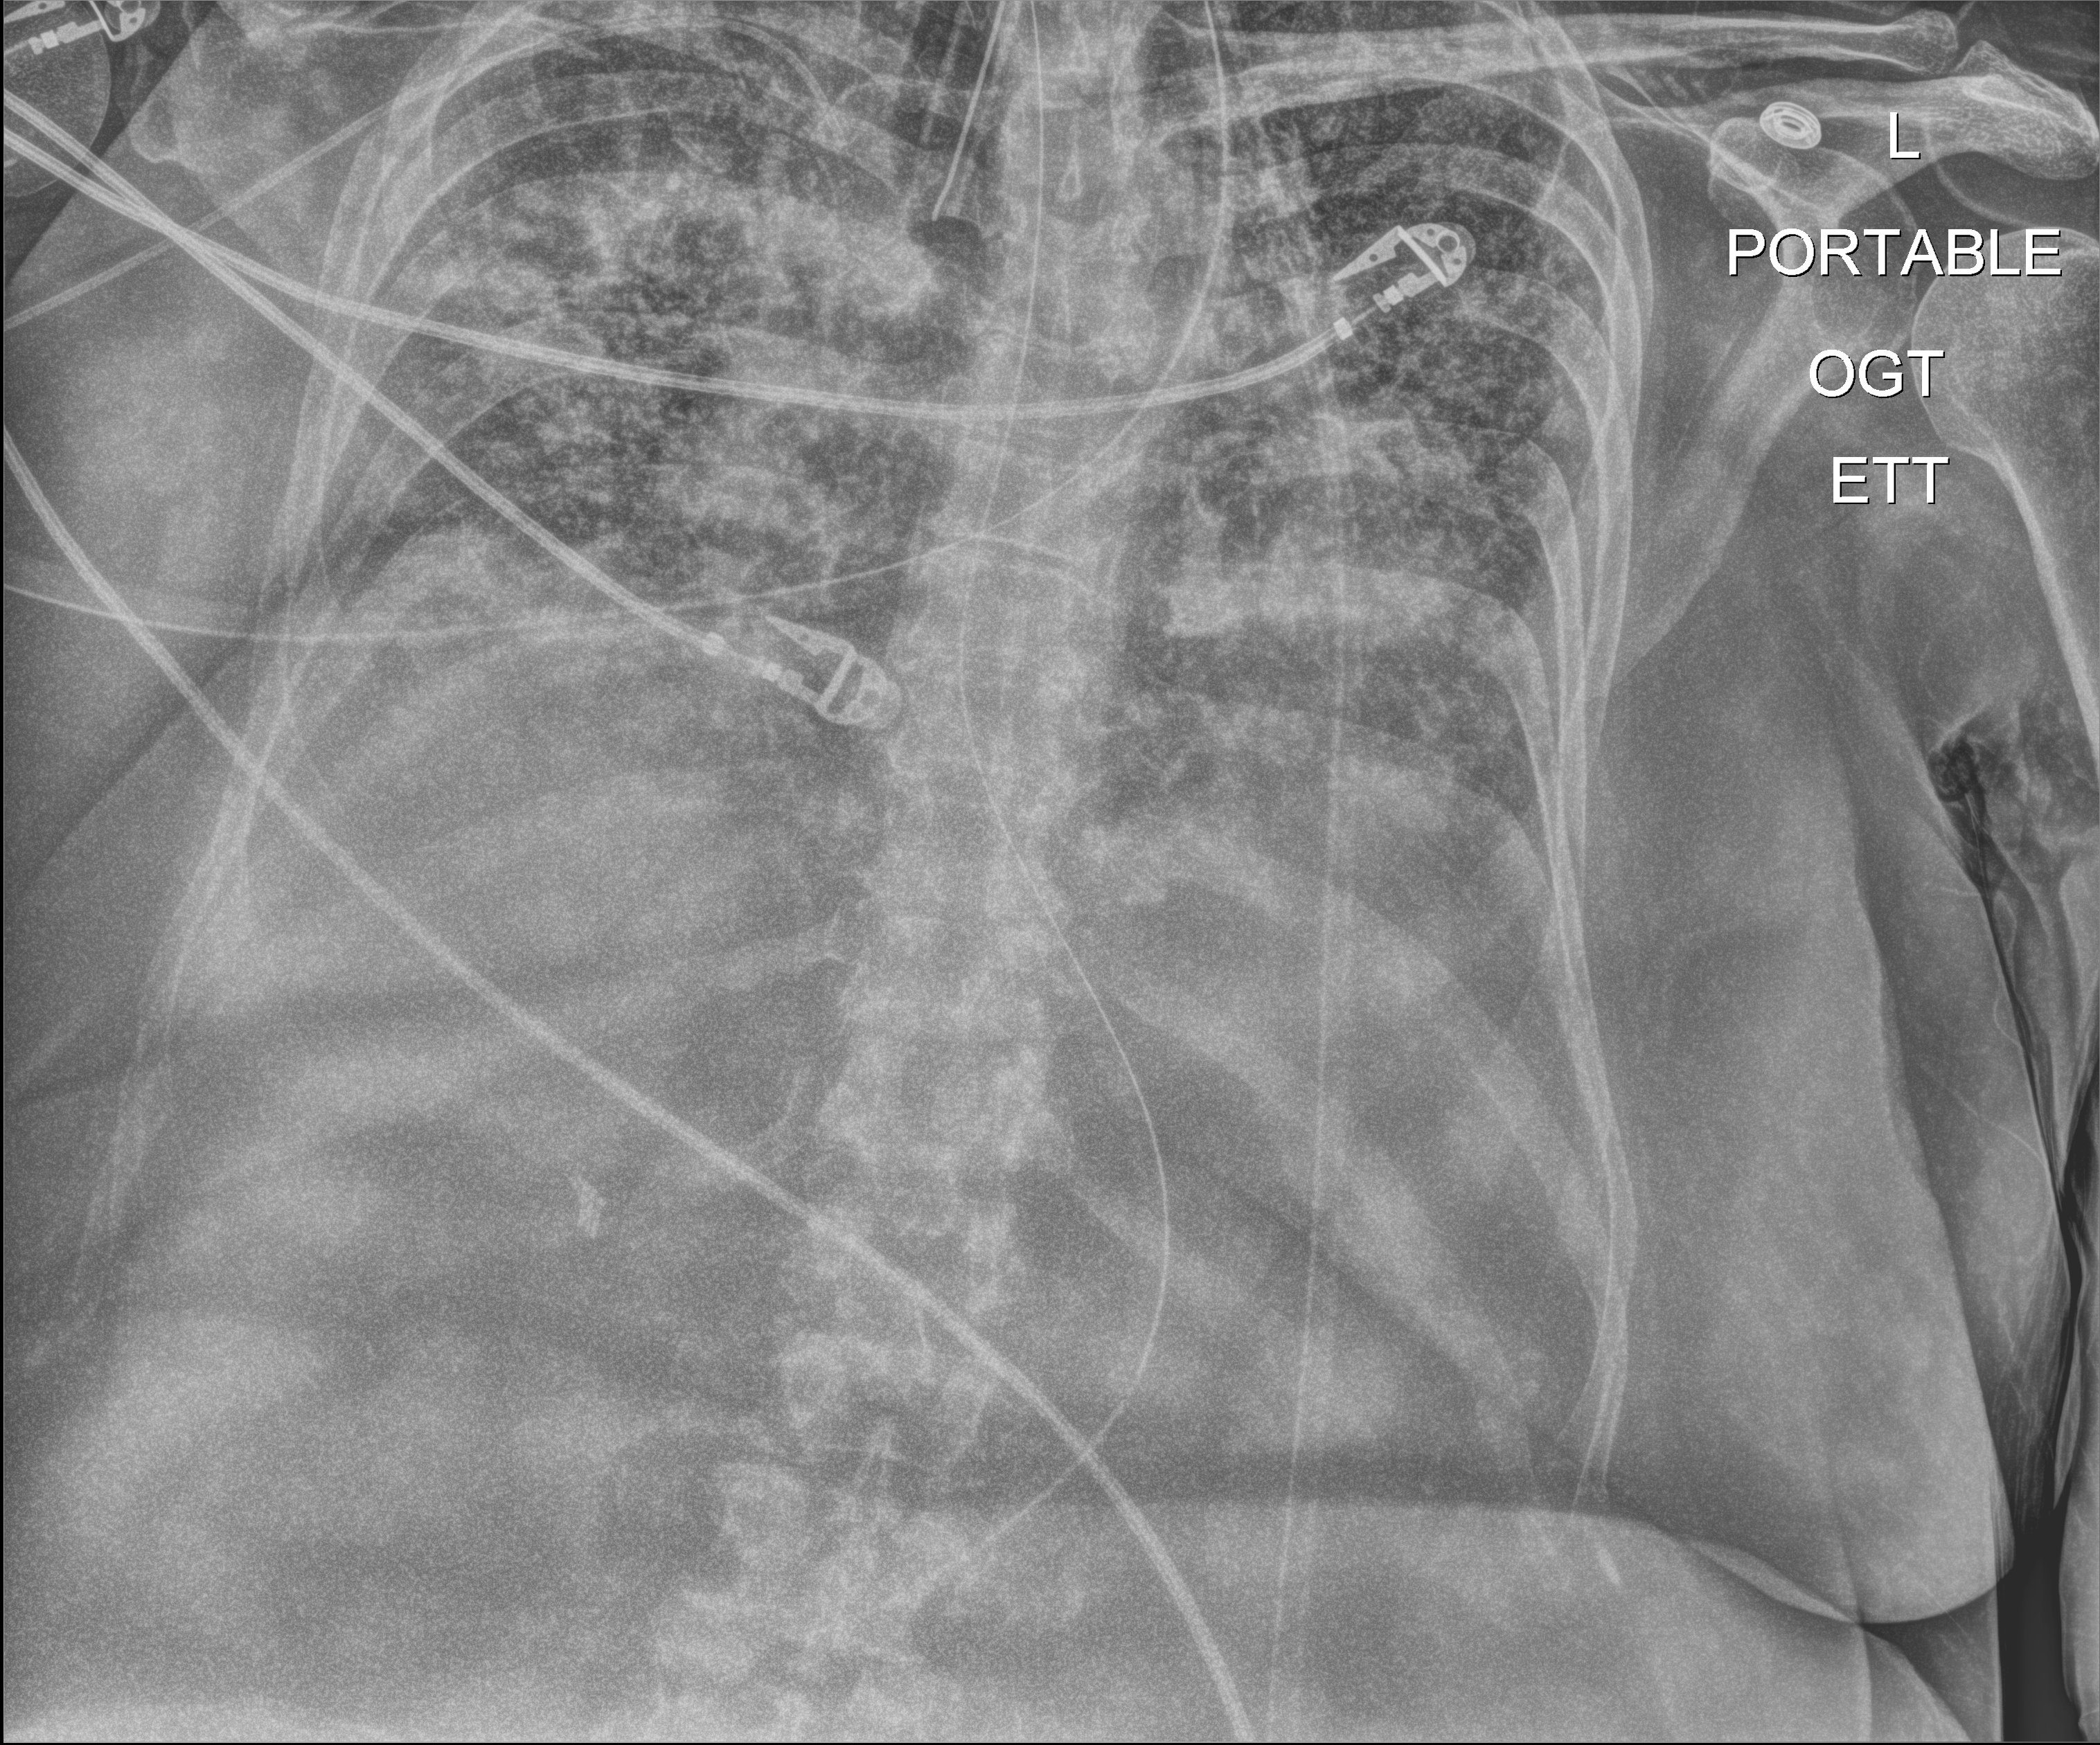
Portable chest radiograph, anteroposterior (AP) projection. Female patient hospitalised with COVID-19, age 60–74 years.
Admission-level facts for this patient (not findings on this image; timing relative to this image not recorded):
- mechanically ventilated during this hospital stay: yes